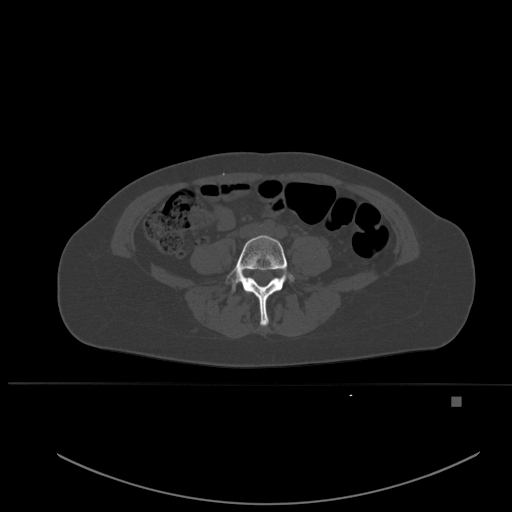
CT including the spine, one axial slice; slice 172 of 651 in the series (ordered by position); bone window (W 1800 / L 400 HU); 1.5 mm slice thickness; 512 × 512 image matrix, field of view 443 × 443 mm. Female patient, age 49 years. Case-level facts recorded for this patient, not image findings: primary cancer: breast; vertebrae with lytic lesions (as recorded): L3, T12, L4.
Annotated regions visible in this slice (semi-automatically segmented with operator editing):
- L4 vertebra: bounding box (x1, y1, x2, y2) in pixels: (225, 235, 294, 326)